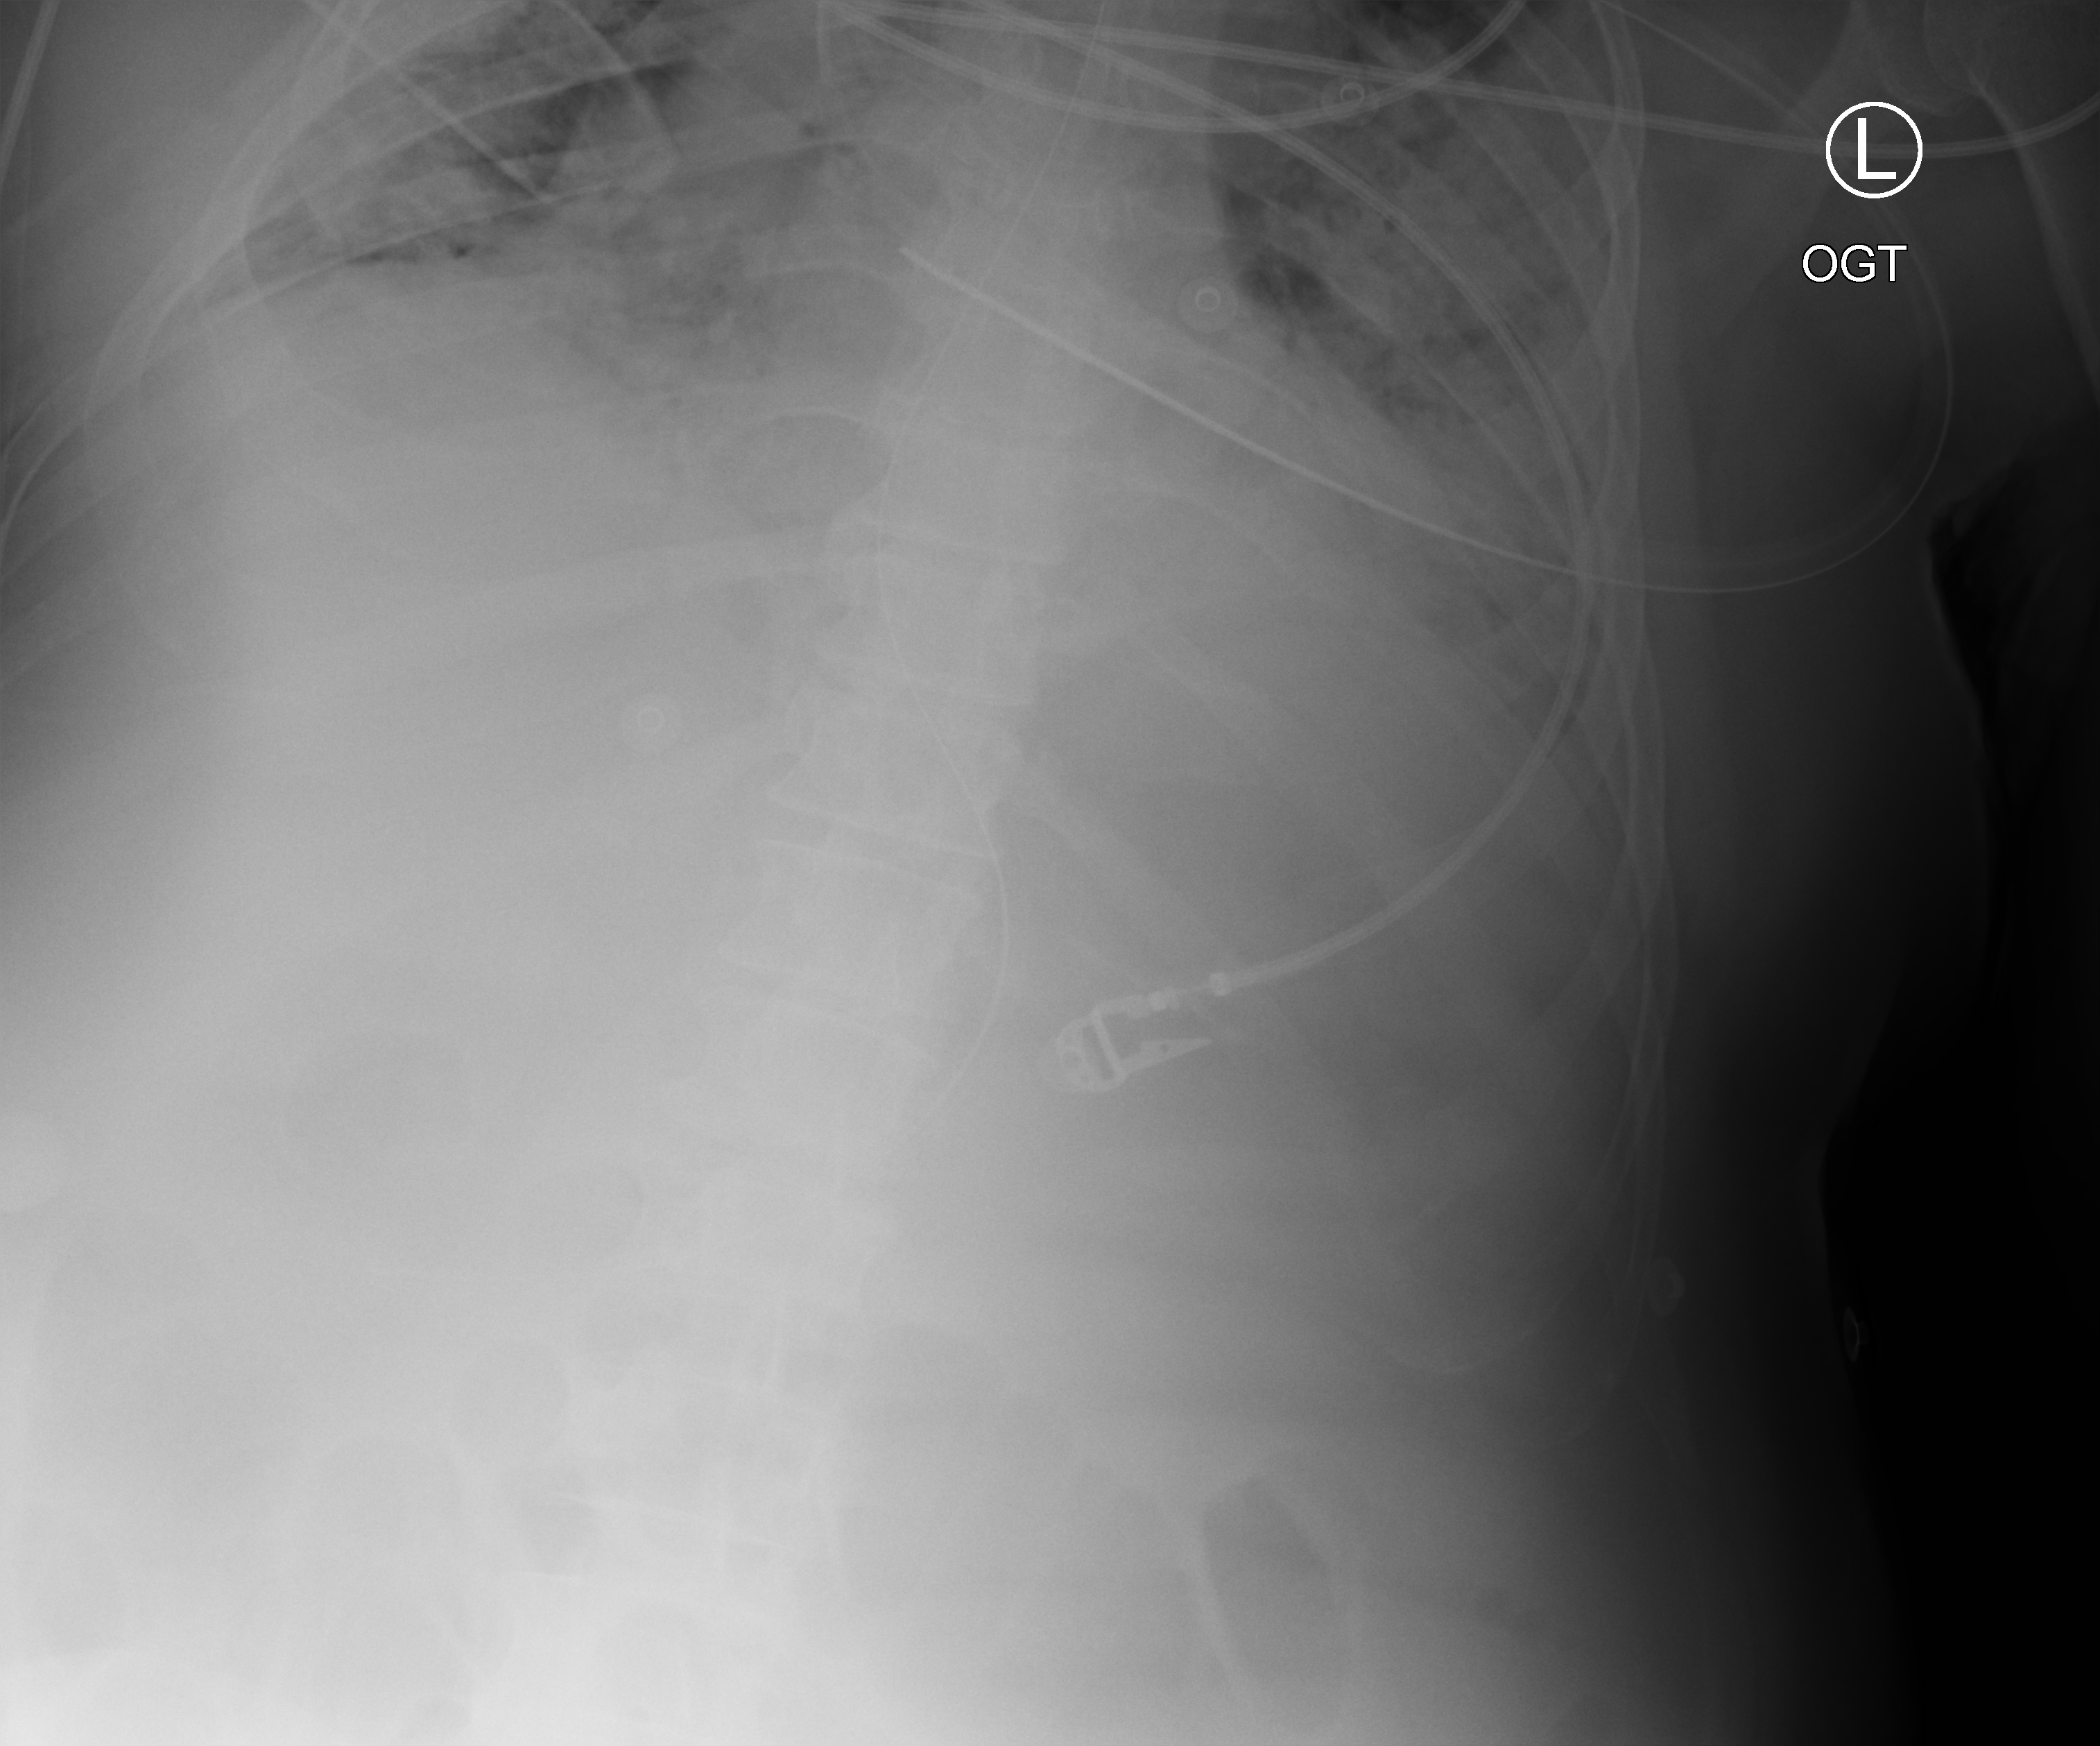
Portable chest radiograph; anteroposterior (AP) projection. Male patient hospitalised with COVID-19, age 18–59 years.
From the hospital-stay record, not from the radiograph (when in the stay this image was taken is not recorded): admitted to intensive care during this hospital stay: yes; diabetes (admission record): no.